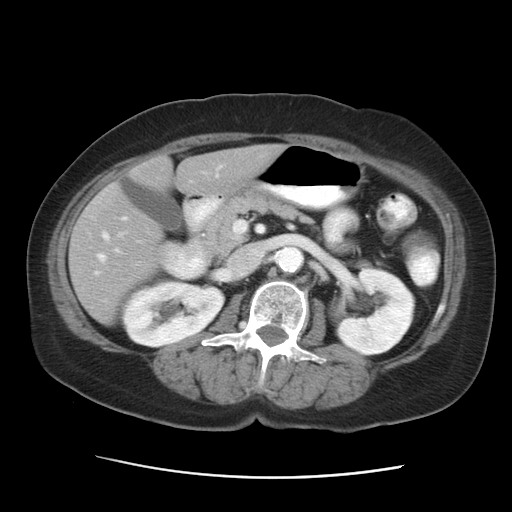
Contrast-enhanced abdominal CT, one axial slice; slice 13 of 29 in the series (ordered by position); reconstruction kernel STANDARD; 120 kVp; intravenous contrast given; soft-tissue window (W 400 / L 40 HU); 7.5 mm slice thickness; 512 × 512 image matrix, field of view 354 × 354 mm. Female patient, age 64 years. From the clinical record (not read from this slice): diagnosis: colorectal cancer liver metastases, imaged before liver resection.
Annotated regions visible in this slice (expert manual segmentation):
- hepatic veins: bounding box [x1, y1, x2, y2] px = [97, 232, 109, 261]
- liver: [69, 145, 283, 324]
- planned liver remnant (the part of the liver to remain after resection): [69, 145, 283, 324]
- portal vein (with intrahepatic branches): [122, 217, 237, 239]